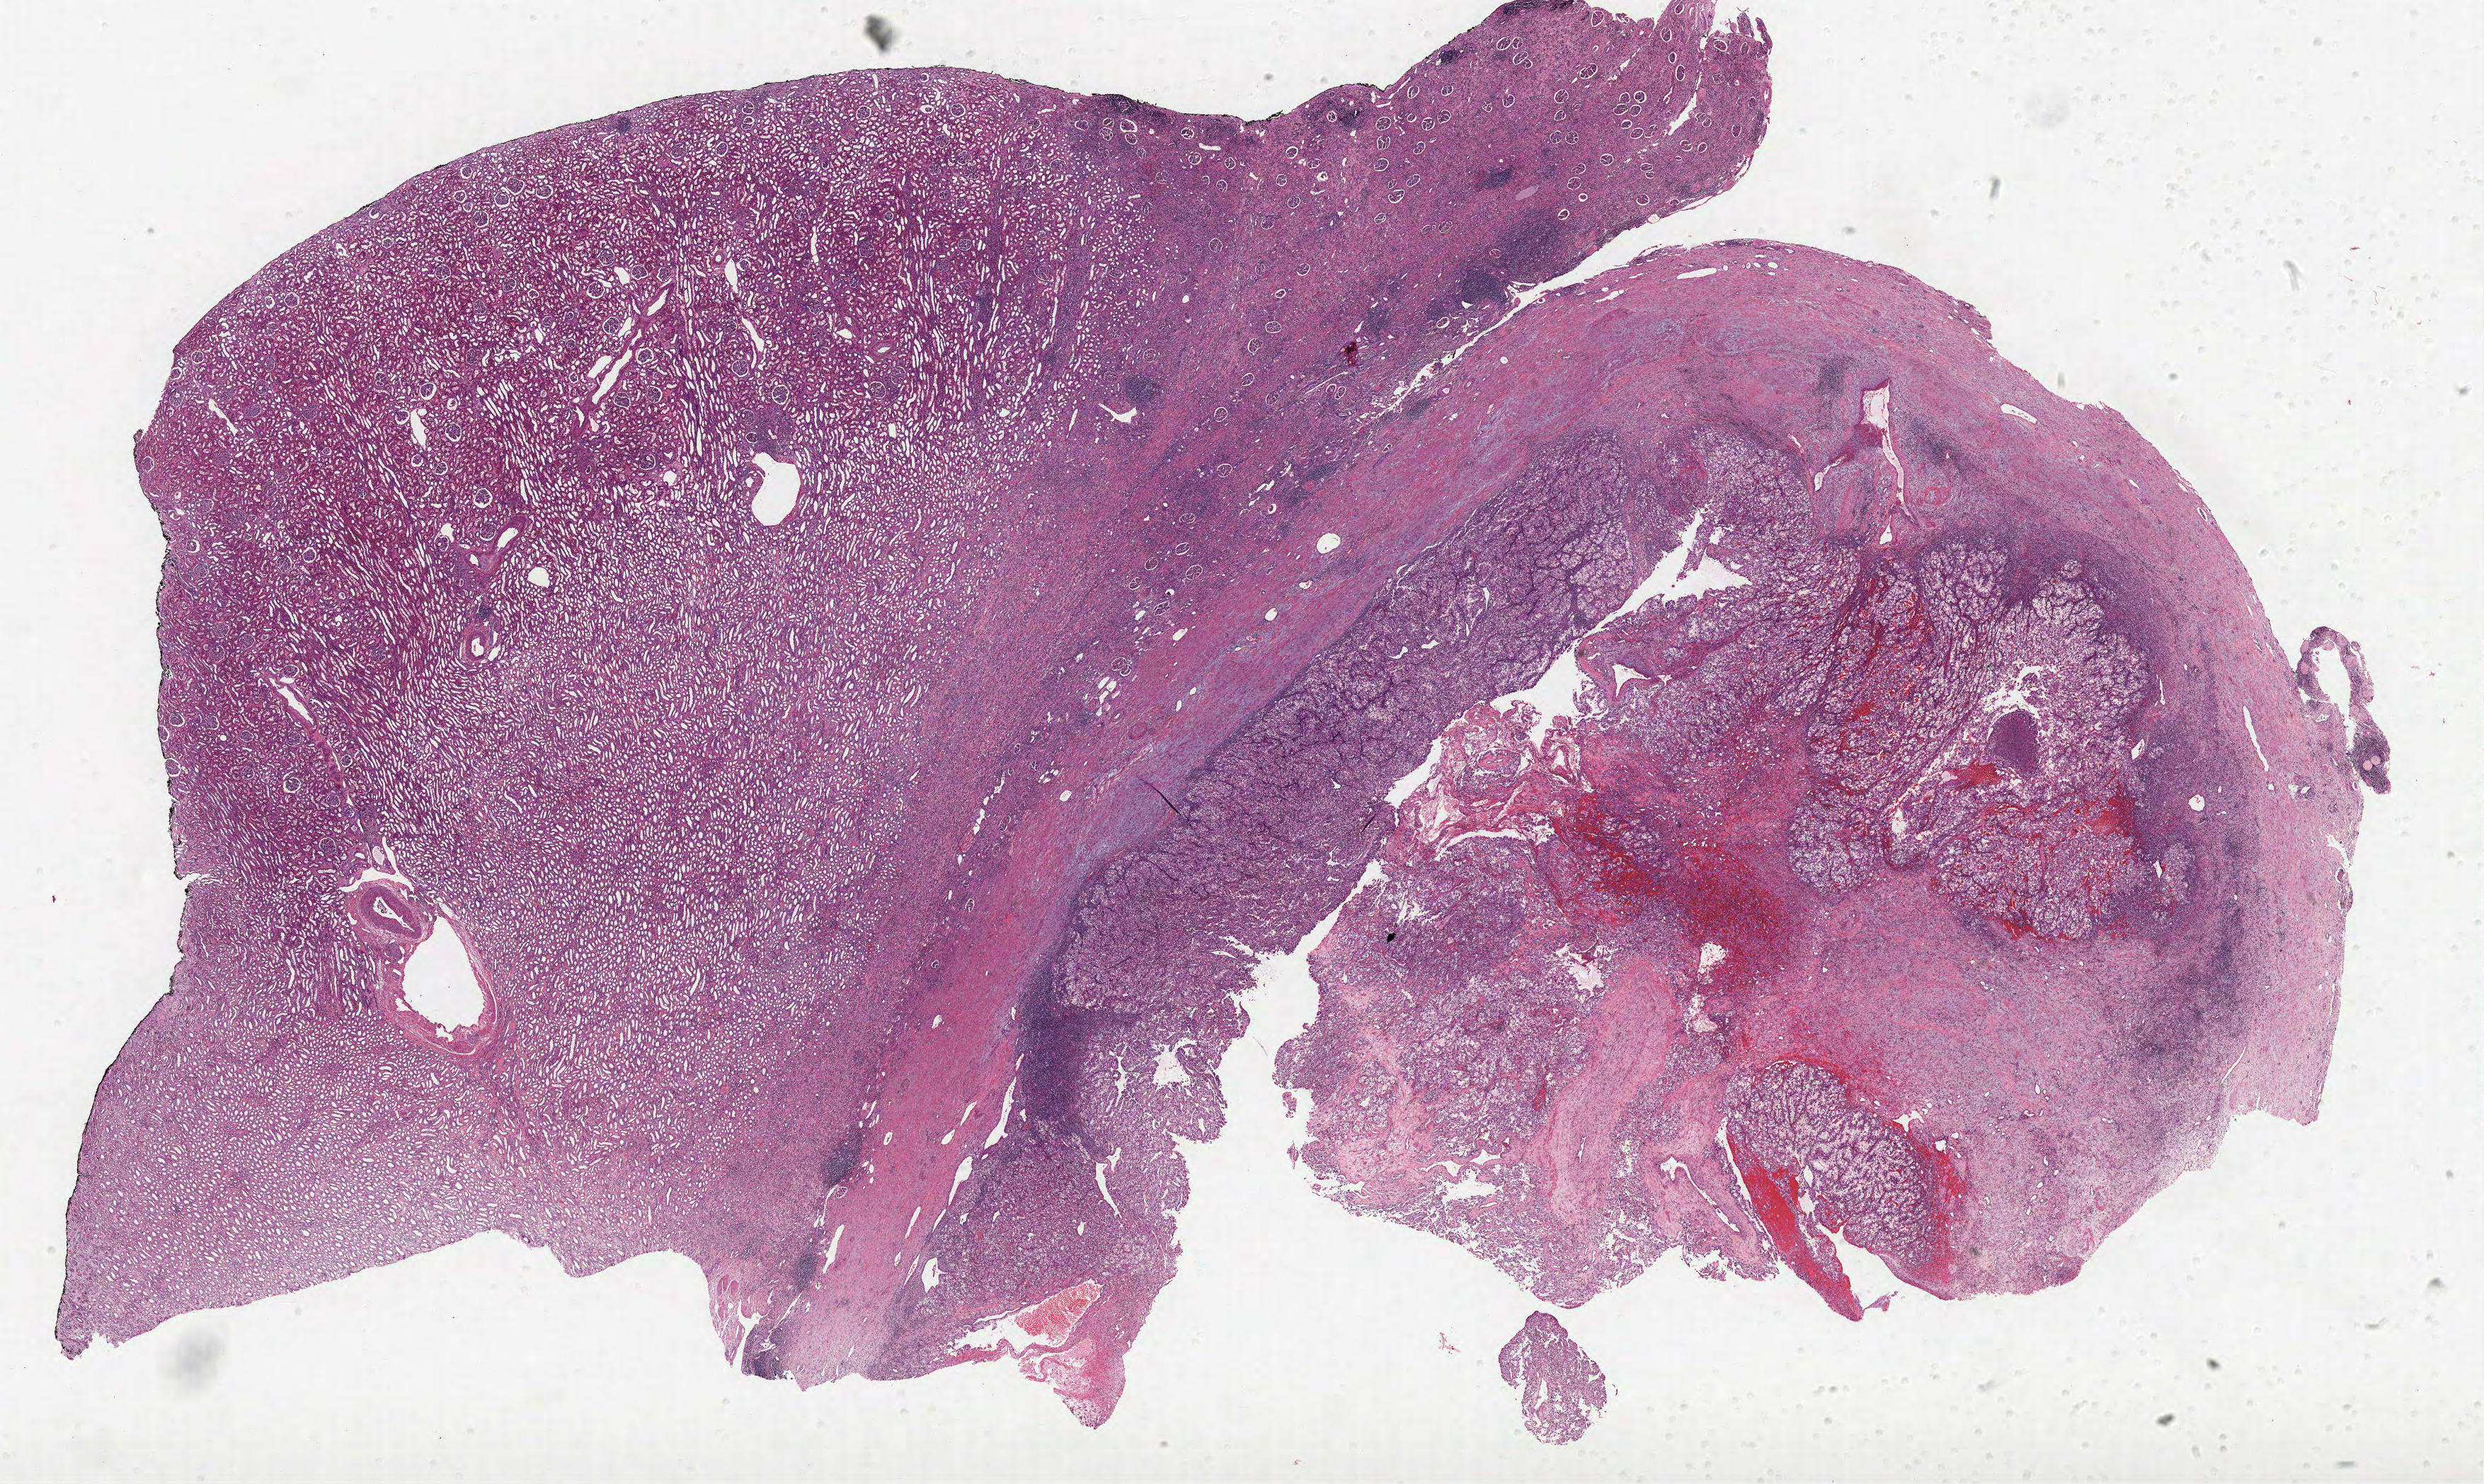
Whole-slide histology image, H&E-stained, whole scanned area (about 28.1 x 16.8 mm) shown as a low-resolution overview; FFPE section; sample: primary tumour, kidney. Patient: male, age at initial diagnosis 60 years. Histologic grade: G3 (poorly differentiated).
* AJCC pathologic stage: I
* TNM: T1a NX M0
* pathologic diagnosis: Clear cell adenocarcinoma, NOS
* laterality: right